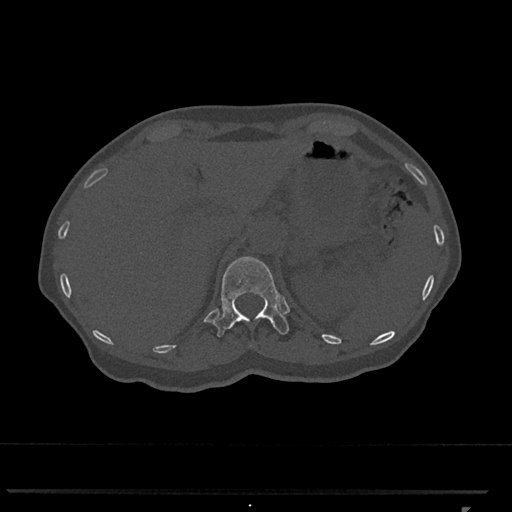
CT including the spine, one axial slice; position 468 of 793 along the scan axis; 120 kVp; bone window (W 1800 / L 400 HU); 0.5 mm slice thickness; 512 × 512 image matrix. Patient: female, 62 years. Case-level facts recorded for this patient, not image findings: primary cancer: renal.
Annotated regions visible in this slice (semi-automatically segmented with operator editing):
- T12 vertebra: bounding box (x1, y1, x2, y2) in pixels: (212, 256, 289, 337)